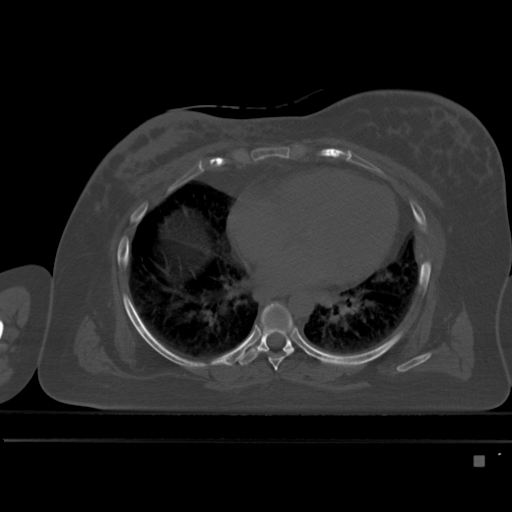
CT including the spine, one axial slice. Position 298 of 495 along the scan axis. Bone window (W 1800 / L 400 HU). 1.5 mm slice thickness. 512 × 512 image matrix, field of view 404 × 404 mm. Female patient, age 33 years. From the clinical record (not read from this slice): primary cancer: breast; vertebrae with lytic lesions (as recorded): T1.
Structures marked on this image (semi-automatic segmentation, software-assisted and operator-edited):
- T6 vertebra: bounding box <258,309,295,371> (left, top, right, bottom; pixels)
- T7 vertebra: <242,303,294,365>